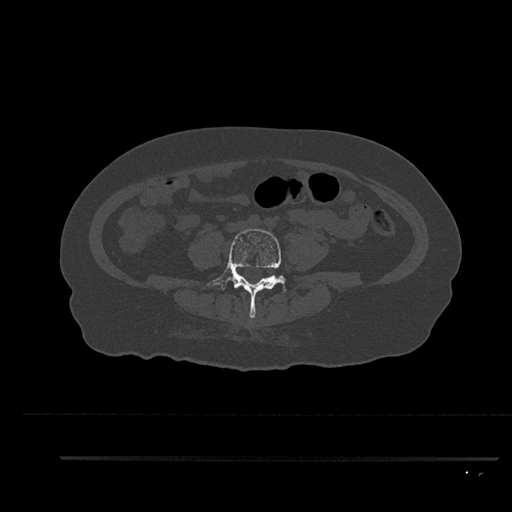
CT including the spine, one axial slice. Position 19 of 797 along the scan axis. 120 kVp. Bone window (W 1800 / L 400 HU). 0.5 mm slice thickness. 512 × 512 image matrix. Patient: female, 44 years. From the clinical record (not read from this slice): primary cancer: renal; vertebrae with lytic lesions (as recorded): L1.
Structures marked on this image (semi-automatic segmentation, software-assisted and operator-edited):
- L4 vertebra: box from (x=207, y=229) to (x=286, y=319) px